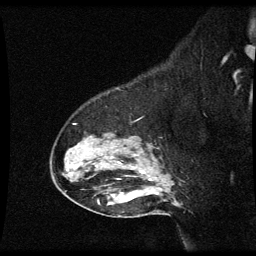
Breast MRI (dynamic contrast-enhanced), one sagittal slice; slice 44 of 60 in the series (ordered by position); dynamic contrast-enhanced series, image 2 of 3 at this slice position (ordered by acquisition); 1.5 T; TE 4.2 ms, TR 8.9 ms; 2 mm slice thickness; 256 × 256 image matrix. Female patient, age 49 years. From the clinical record (not read from this slice): setting: breast cancer imaged before/during neoadjuvant chemotherapy; receptor status: HR-positive, HER2-negative.
Annotated regions visible in this slice (semi-automatic segmentation, software-assisted and operator-edited):
- analysis volume of interest (the breast-tissue region the enhancement analysis was run in; not a lesion): bounding box [x1, y1, x2, y2] px = [52, 122, 177, 205]
- tumour enhancement mask (voxels above the 70 % enhancement threshold inside the analysis volume of interest): [142, 172, 145, 175]